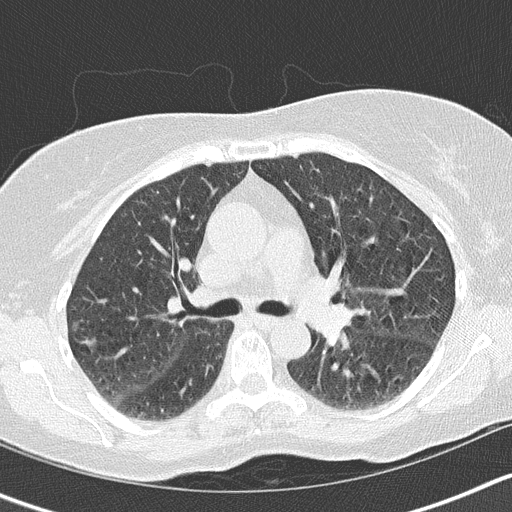
Axial slice from a low-dose chest CT screening exam, baseline annual screen, lung window (W 1500 / L -600 HU), 2 mm slice thickness, slice 55 of 148 in the series, 512 × 512 image matrix. Female participant, aged 61 years at enrolment. Current smoker at enrolment.
Lesion marked by an expert reader, bounding box <65,318,122,365> (left, top, right, bottom; pixels). No non-calcified nodule or mass ≥4 mm was recorded by the screening reader at this exam.